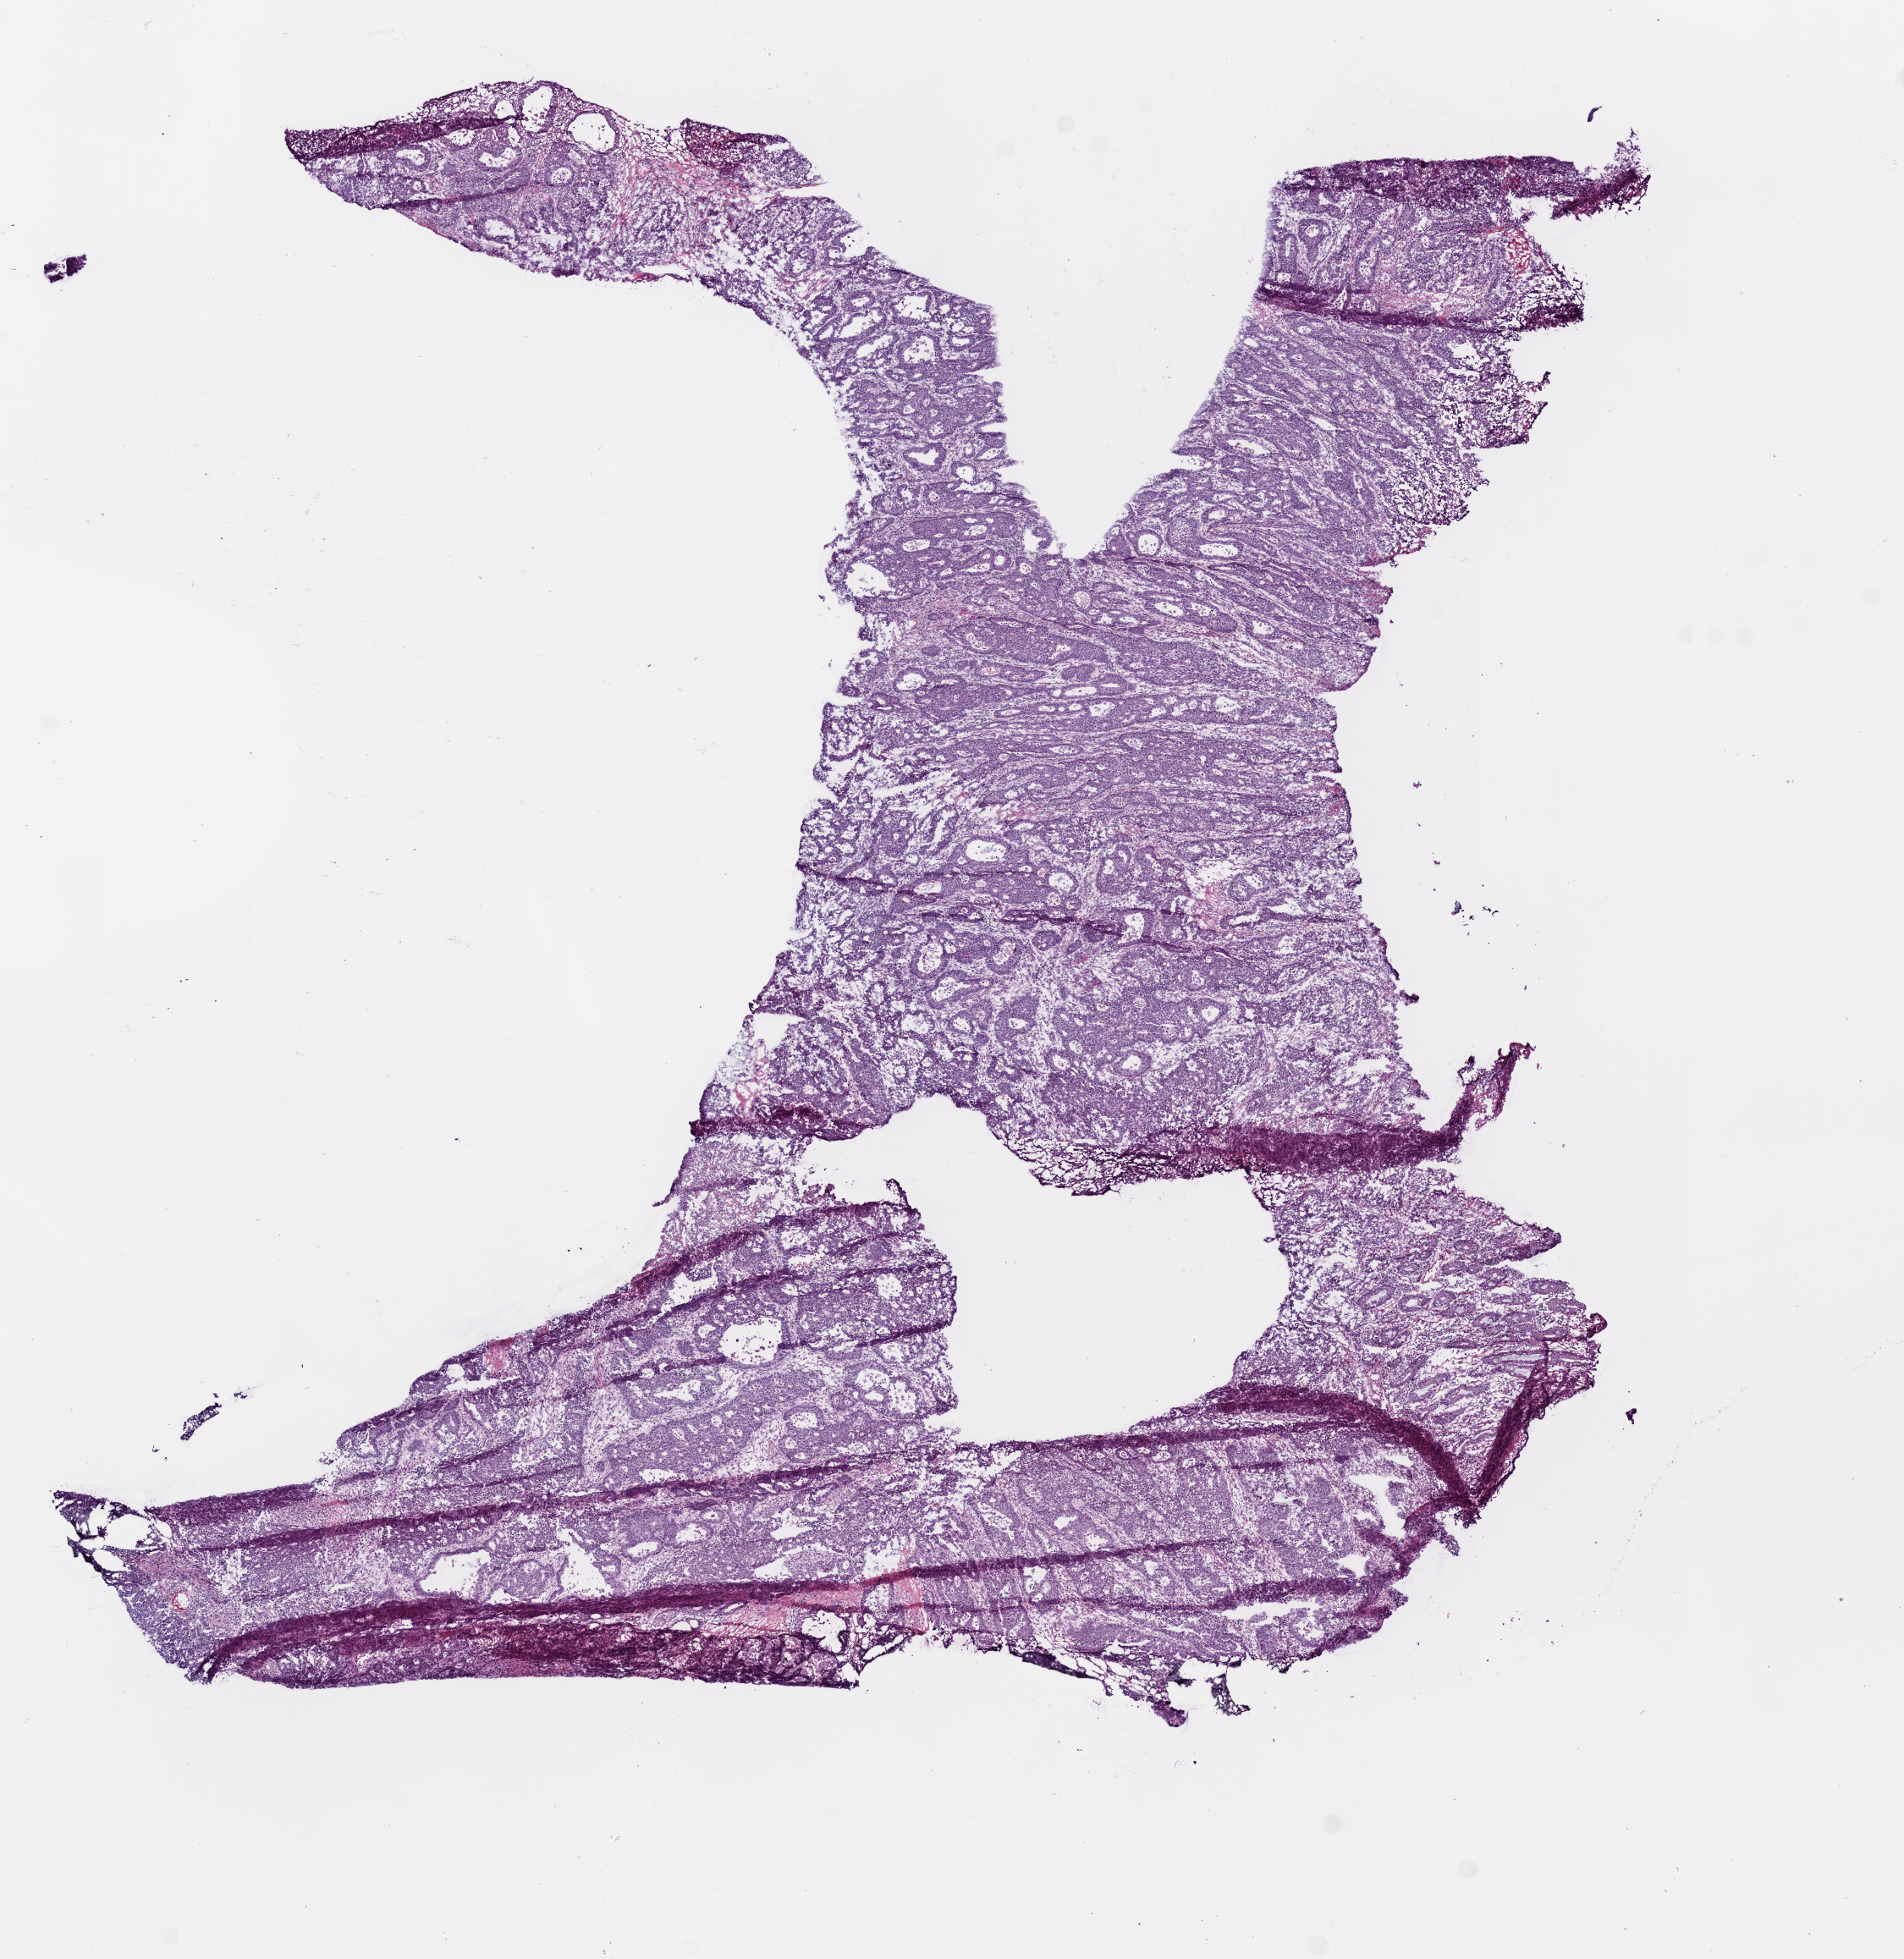
Whole-slide histology image, H&E-stained, whole scanned area (about 9.0 x 9.3 mm) shown as a low-resolution overview; frozen section from the bottom of the tissue portion; primary tumour sample from the colon. Patient: female, age at initial diagnosis 83 years. Pathologist review of this section (percent, as recorded): tumour cells 85%, tumour nuclei 75%, normal cells 0%, stromal cells 10%, necrosis 5%.
• AJCC pathologic stage: II
• lymph nodes positive (case pathology): 0 of 23 examined
• TNM: T3 N0 M0
• diagnosis: Adenocarcinoma, NOS (ascending colon)